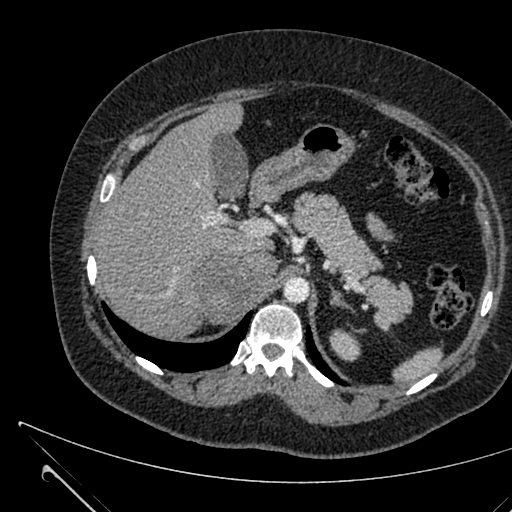
Contrast-enhanced abdominal CT, one axial slice; position 458 of 731 along the scan axis; 120 kVp; soft-tissue window (W 400 / L 40 HU); 1 mm slice thickness; 512 × 512 image matrix. Female patient, age 36 years. Case-level facts recorded for this patient, not image findings: diagnosis: adrenocortical carcinoma; tumour side: right adrenal; tumour size at pathology: 10 cm; Ki-67 index: 20 %; stage (as recorded): 4.
Outlined on this slice (semi-automatically segmented with operator editing):
- mass: box from (x=193, y=253) to (x=277, y=322) px